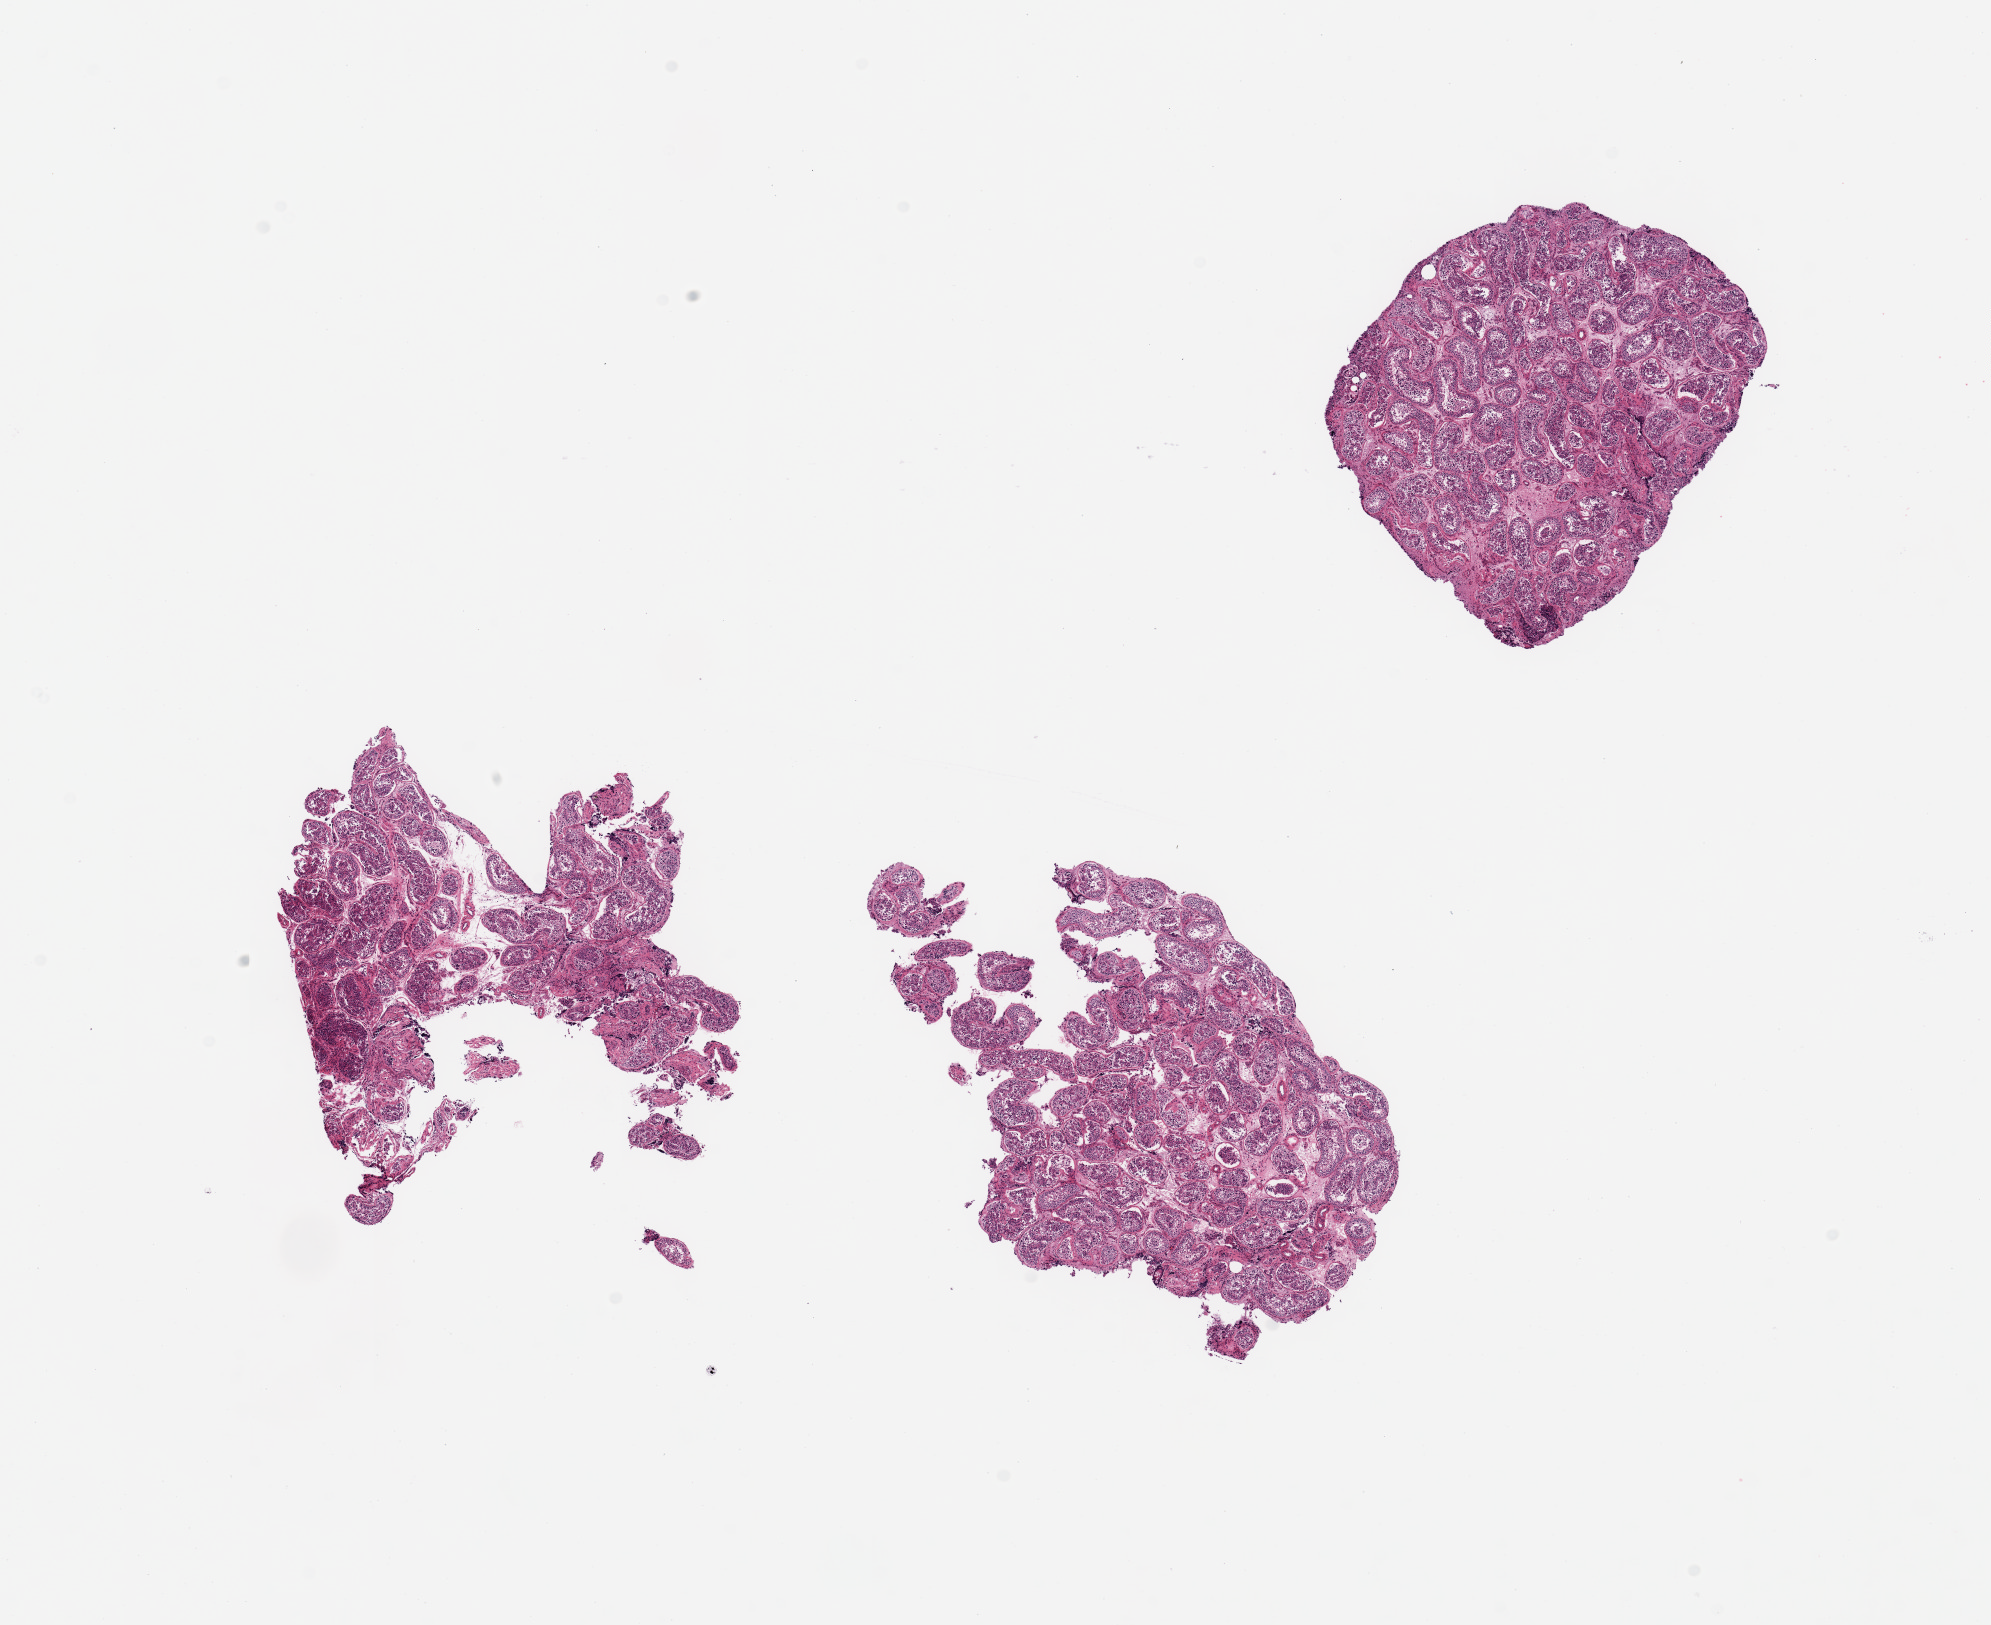
Hematoxylin and eosin (H&E) whole-slide image, shown as a low-resolution overview of the whole scanned area (about 15.8 x 12.9 mm, slide scanned at 20x), PAXgene-fixed, paraffin-embedded tissue, target tissue: testis, tissue donor sample.
Review note (as recorded): 2 pieces, 1 fragmented; active spermatogenesis.